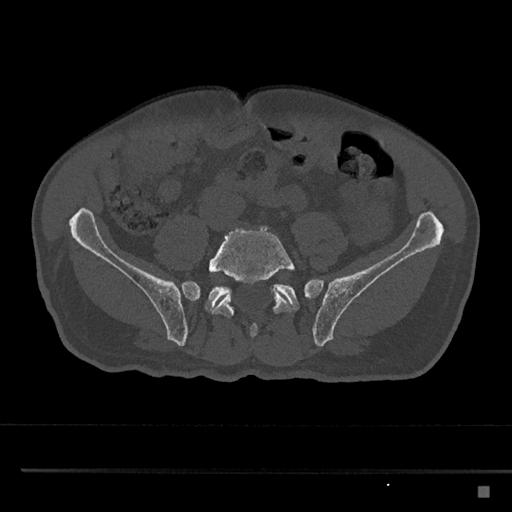
CT including the spine, one axial slice; position 568 of 797 along the scan axis; reconstruction kernel Br40s/3; 120 kVp; bone window (W 1800 / L 400 HU); 0.5 mm slice thickness; 512 × 512 image matrix, field of view 391 × 391 mm. Male patient, age 59 years. From the clinical record (not read from this slice): primary cancer: prostate.
Outlined on this slice (semi-automatic segmentation, software-assisted and operator-edited):
- L5 vertebra: bounding box <208,226,295,337> (left, top, right, bottom; pixels)